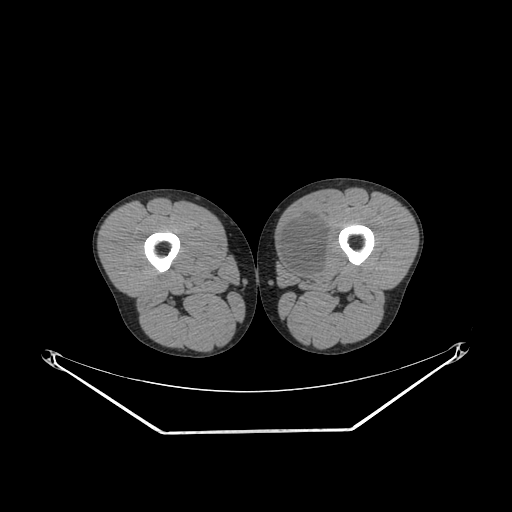
CT of an extremity soft-tissue mass (from a PET/CT study), one axial slice. Slice 241 of 311 in the series (ordered by position). Reconstruction kernel SOFT. Soft-tissue window (W 400 / L 40 HU). 3.75 mm slice thickness. 512 × 512 image matrix, field of view 500 × 500 mm. Male patient. From the clinical record (not read from this slice): histological type: mixoid liposarcoma; grade: low; site of the primary tumour: left thigh.
Structures marked on this image (expert contour drawn on MRI and transferred to this co-registered scan by the dataset authors):
- gross tumour volume (mass): box from (x=279, y=215) to (x=328, y=277) px